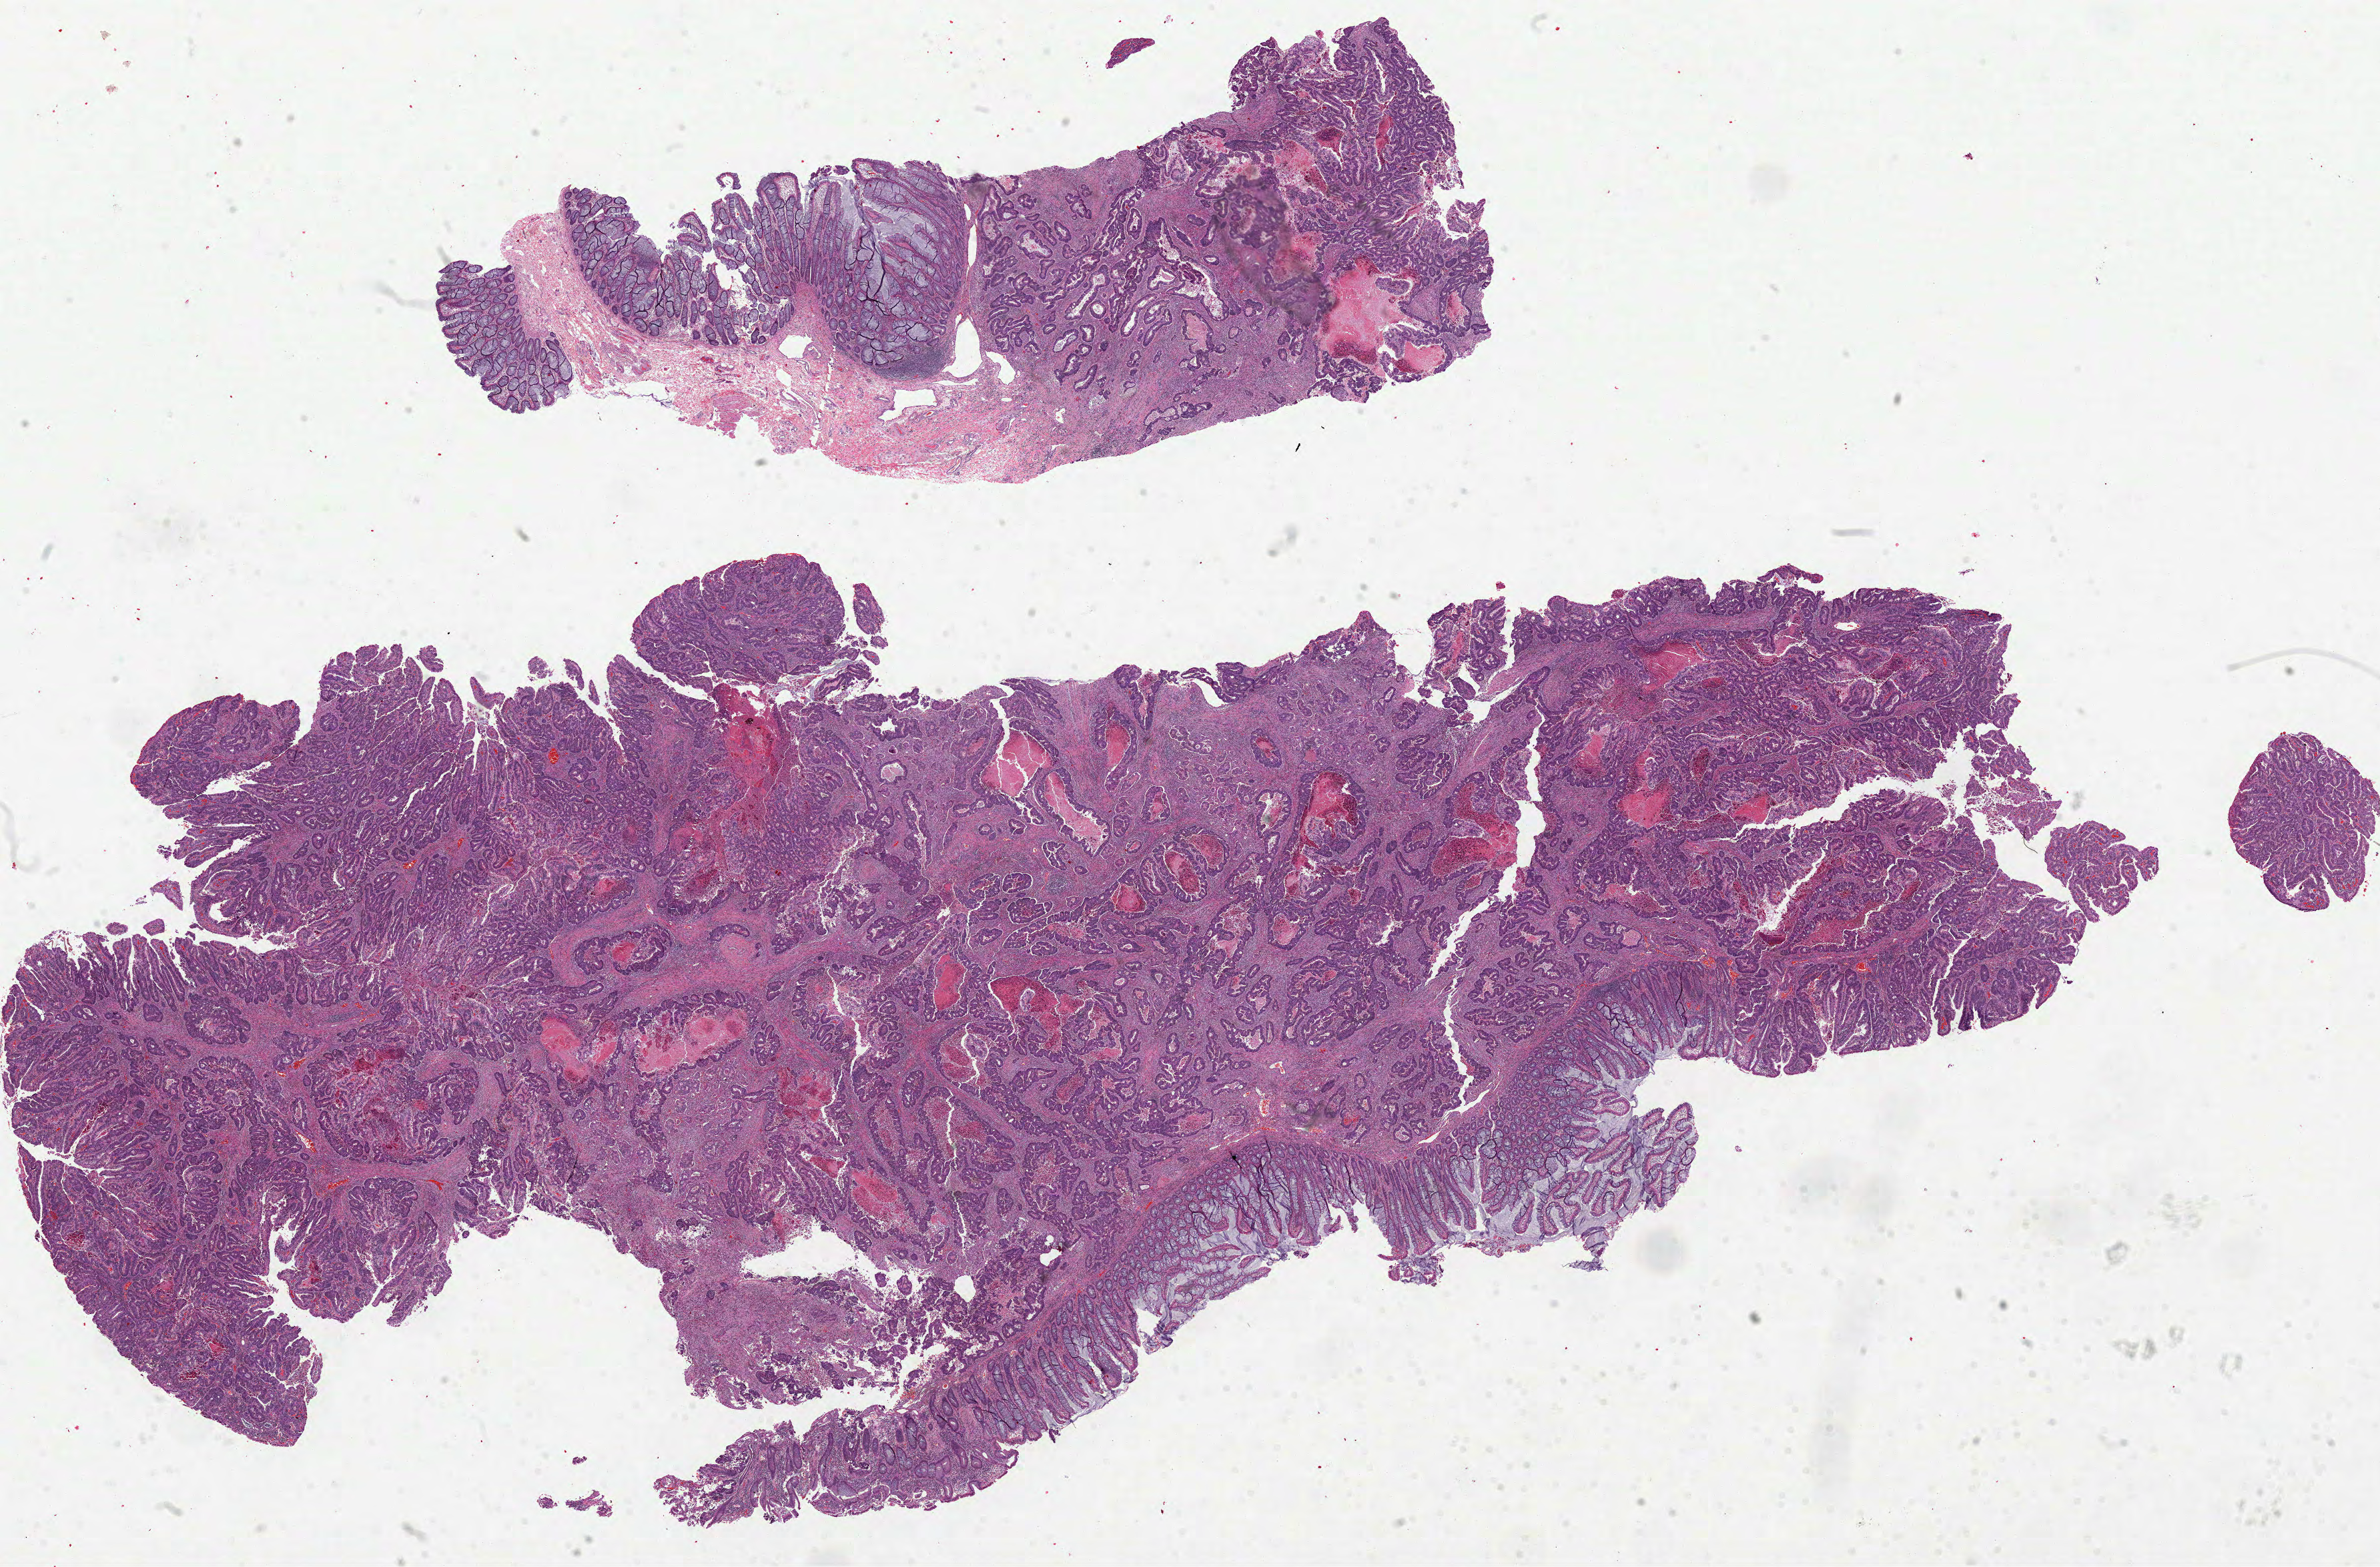
Digitized H&E-stained tissue section (whole slide), a low-resolution overview of the entire scanned area, about 28.8 x 18.9 mm, FFPE section, sample: primary tumour, rectum. Male, age 57 years at initial diagnosis.
Histologic diagnosis: Adenocarcinoma, NOS (rectosigmoid junction). AJCC pathologic stage: I (7th edition).